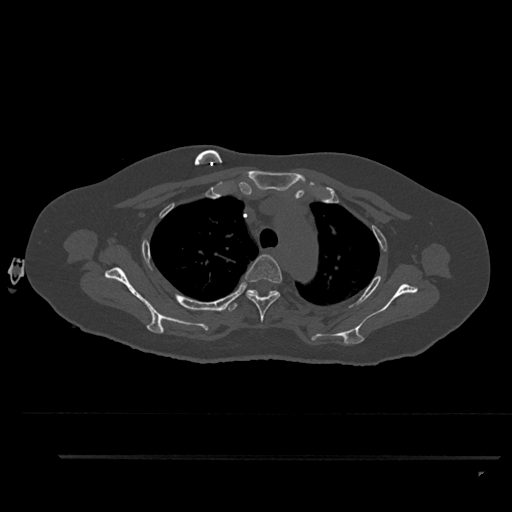
CT including the spine, one axial slice. Position 673 of 797 along the scan axis. Reconstruction kernel Br40s/3. 120 kVp. Bone window (W 1800 / L 400 HU). 512 × 512 image matrix. Female patient, age 44 years. Case-level facts recorded for this patient, not image findings: primary cancer: renal; vertebrae with lytic lesions (as recorded): L1.
Structures marked on this image (semi-automatically segmented with operator editing):
- T3 vertebra: bounding box <244,254,282,322> (left, top, right, bottom; pixels)
- T4 vertebra: <227,289,279,311>